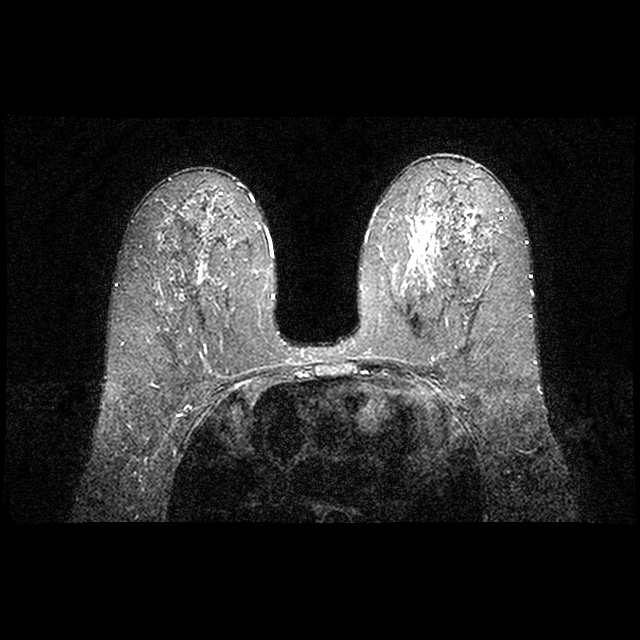
Breast MRI examination; 2 images, each one mid-volume slice chosen by position. Patient in her 40s.
Image 1: fluid-sensitive (T2/STIR) axial slice, series "STIR SENSE", slice 46 of 90.
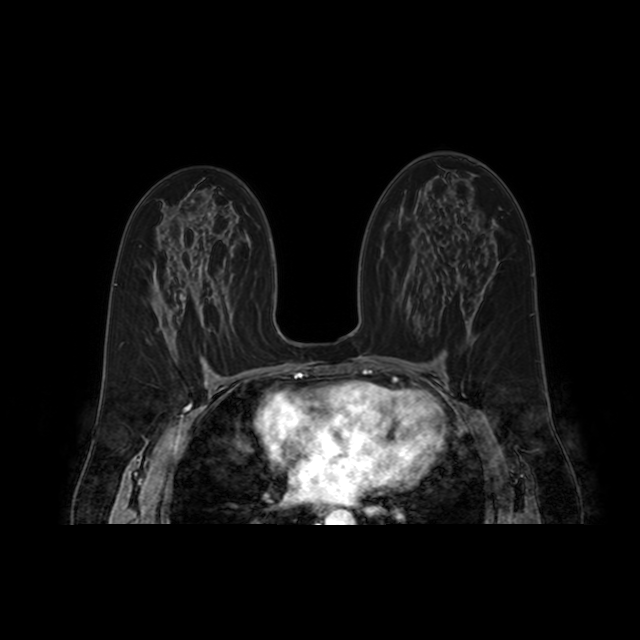
Image 2: axial dynamic contrast-enhanced T1-weighted image, slice 46 of 90, dynamic phase 6 of 10.
MRI impression (as recorded): RIGHT BREAST: There is moderate background enhancement. Within the lower, central right breast at 6-7:00 position is an irregularly marginated, bilobed, enhancing mass which measures 2.1 x 2.0 x 4.6 cm. There is a biopsy clip along within the center and slightly medial portion of the mass. The mass demonstrates rapid and persistent enhancement. No areas of architectural distortion are seen within the right breast. There is no skin thickening, nipple inversion, or right axillary lymphadenopathy present. IMPRESSION: 1) 4.5 cm bilobed, irregularly marginated, enhancing mass in the lower, central right breast with marking clip located centrally within the mass consistent with recent biopsy proven lobular carcinoma. 2) No evidence of right axillary lymphadenopathy. 3) No evidence of malignancy in the left breast; BI-RADS 6.
Pathology recorded for this patient (not read from these images): pathology diagnosis: infiltrat lobular (right breast); receptor status (as recorded): ER pos, PR neg (stain moderate), HER2 neg; pathology report notes: re-bx single 1cm residual CA focus.